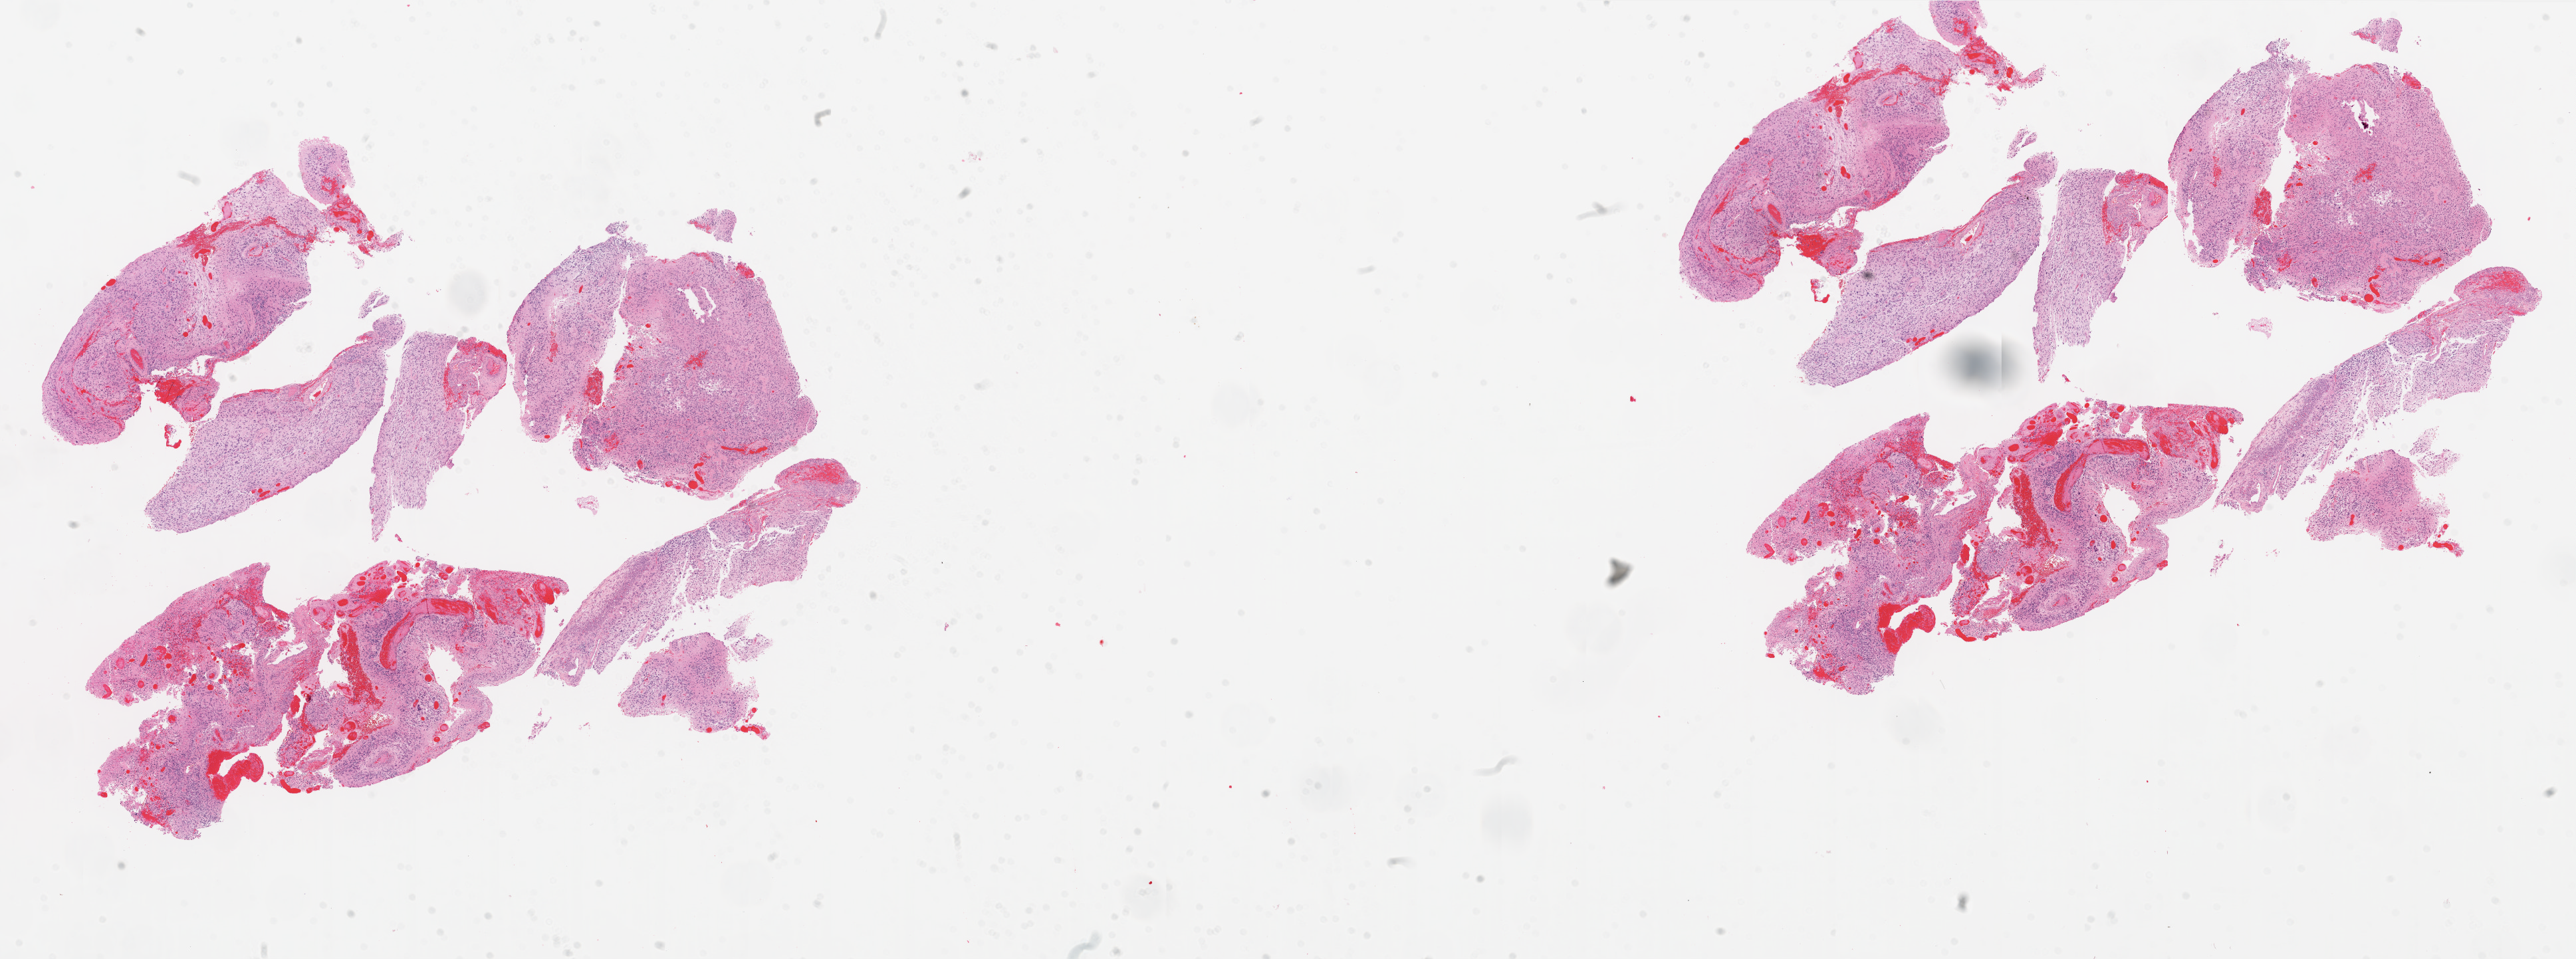
H&E whole-slide image — whole scanned area (about 31.1 x 11.6 mm) shown as a low-resolution overview. Frozen section from the top of the tissue portion. Primary tumour sample from the brain. Patient: male, age at initial diagnosis 52 years. Composition of this section per pathologist review: tumour cells 99%, tumour nuclei 80%, normal cells 0%, stromal cells 0%, necrosis 1%.
Diagnosis: Glioblastoma.